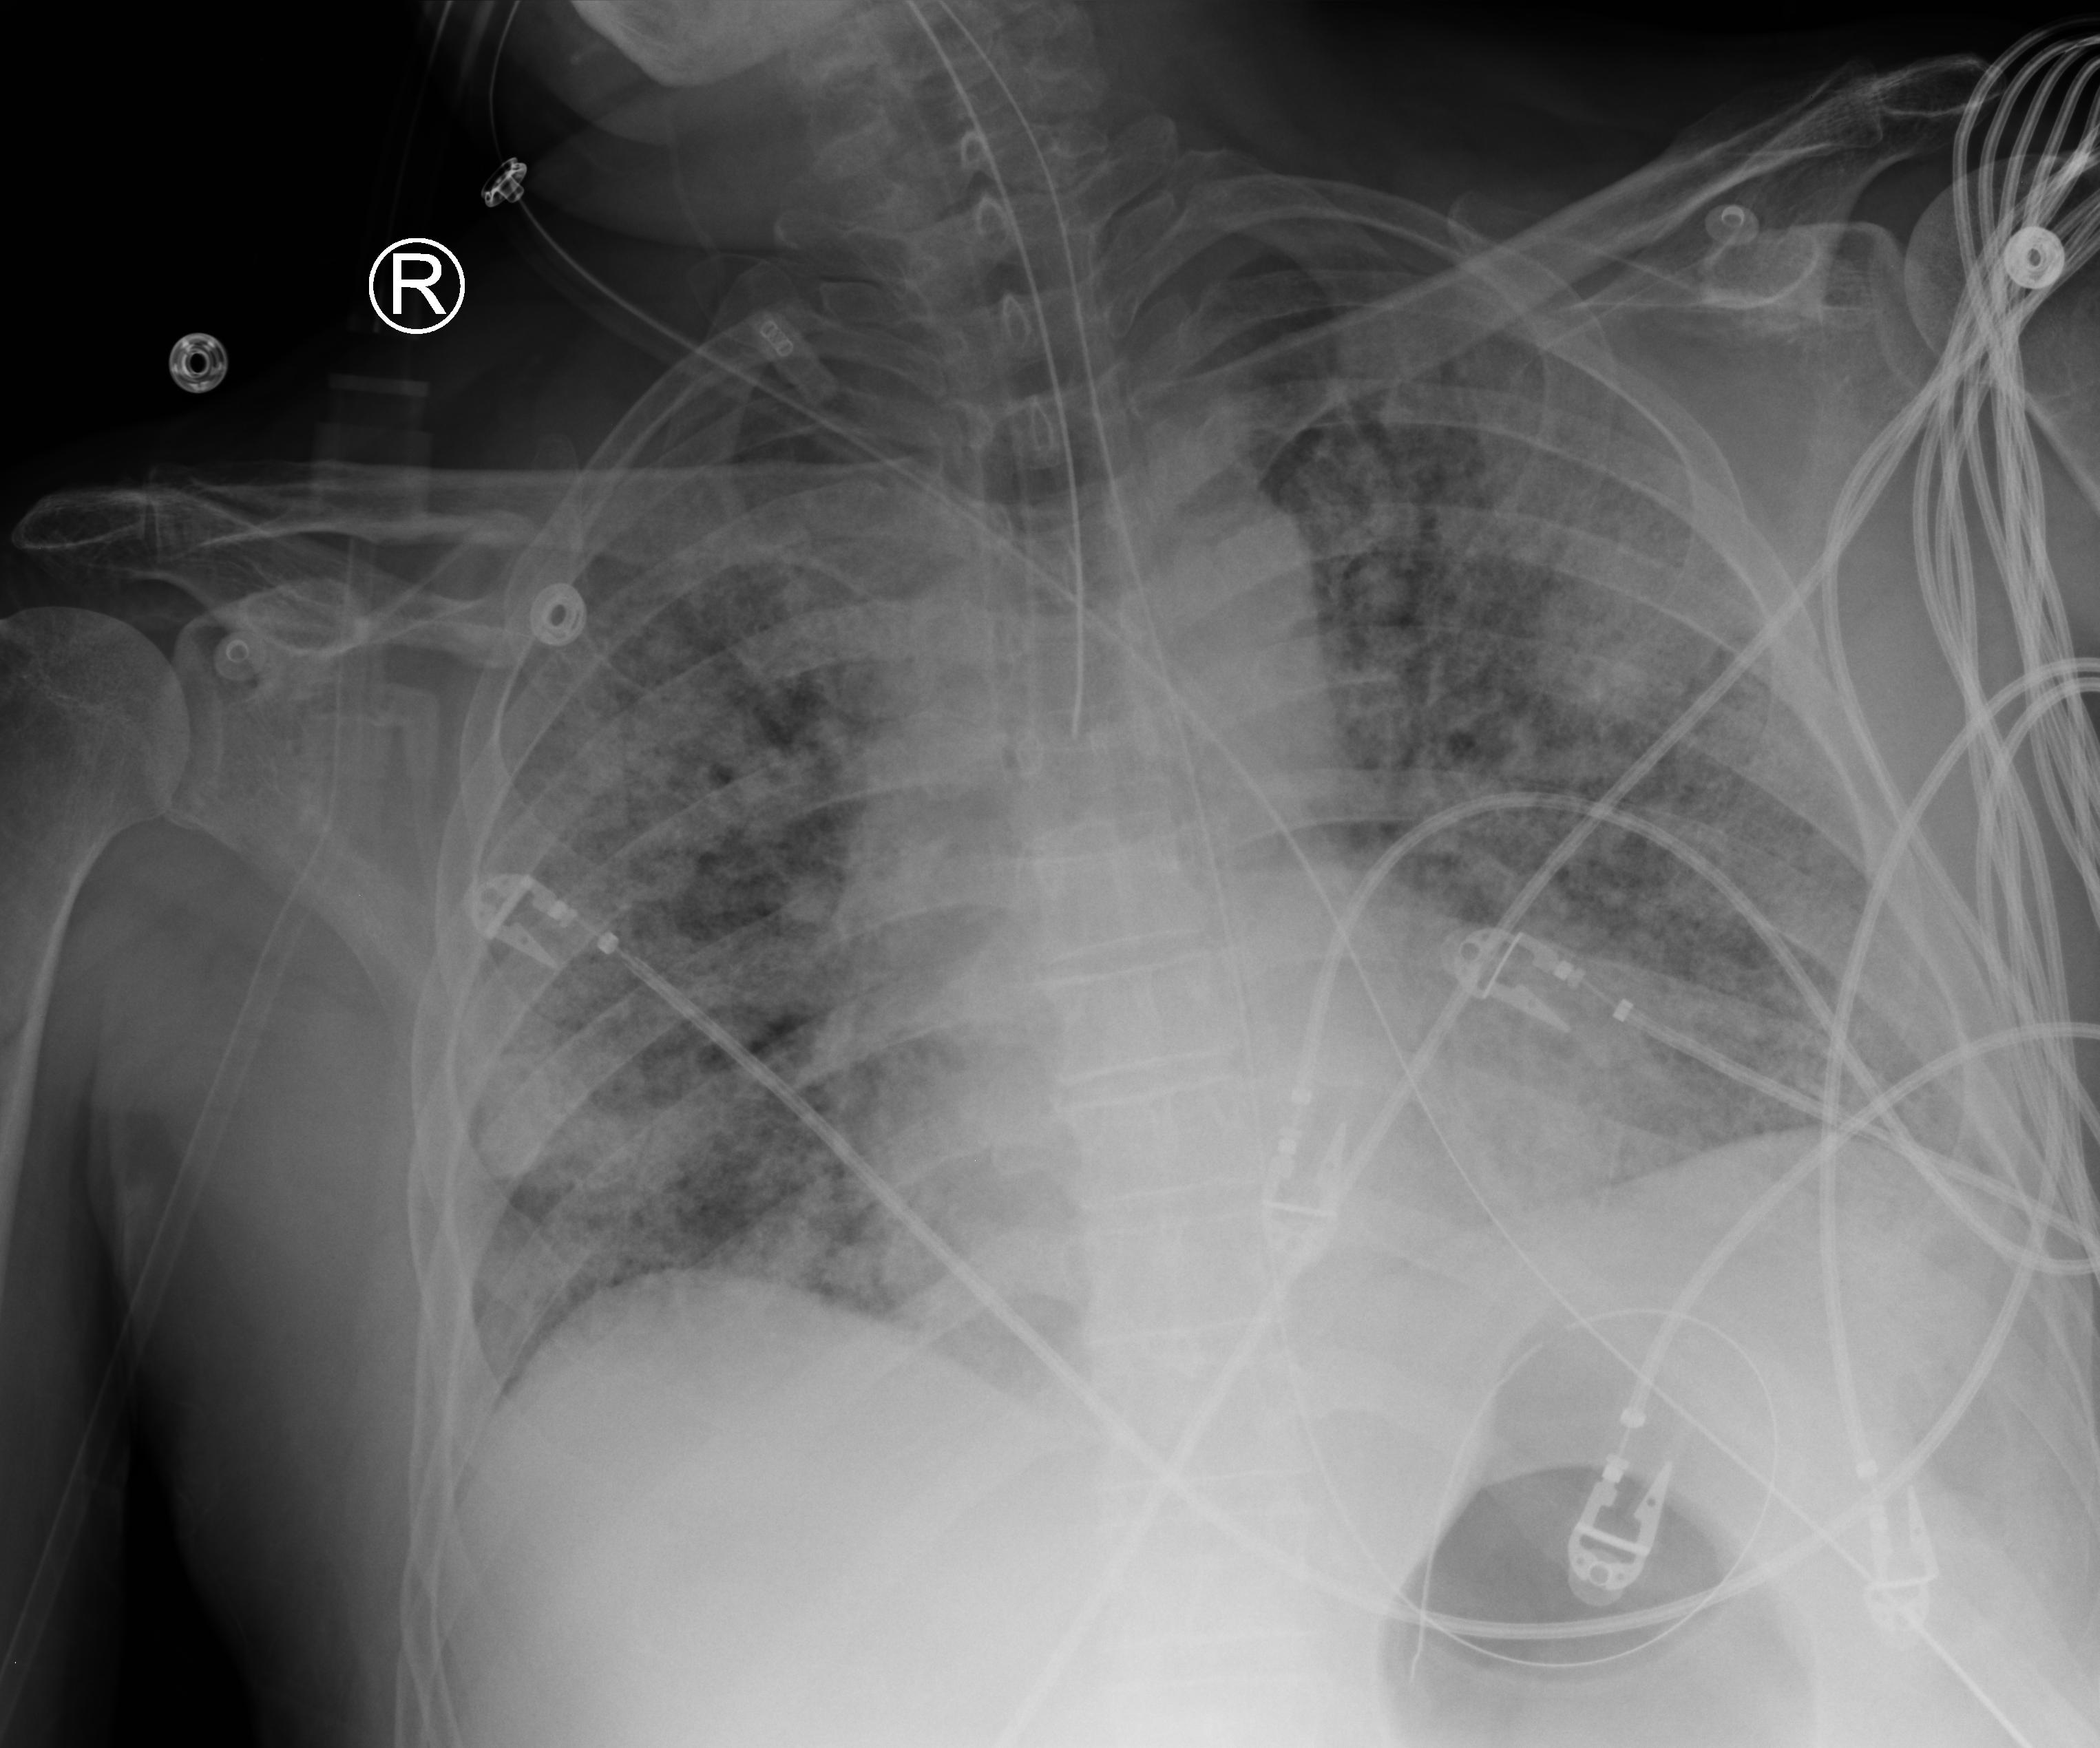
Portable chest radiograph; anteroposterior (AP) projection. Male patient hospitalised with COVID-19, age 60–74 years.
Hospital-stay facts (about this admission, not read from this image; timing relative to this image not recorded): mechanically ventilated during this hospital stay: yes.